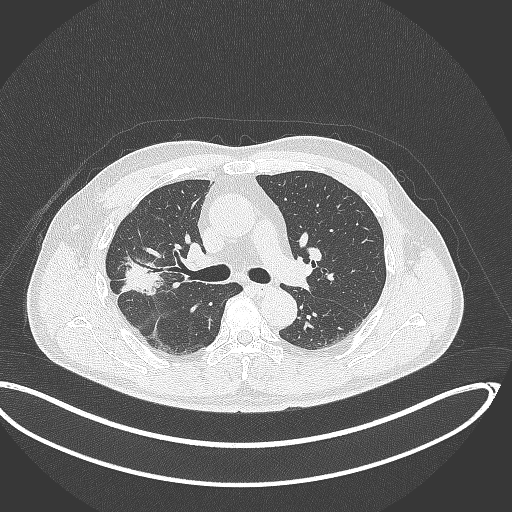
Chest CT, one axial slice; position 212 of 391 along the scan axis; 120 kVp; lung window (W 1500 / L -600 HU); 512 × 512 image matrix, field of view 439 × 439 mm. Patient: male, 63 years. From the clinical record (not read from this slice): clinical TNM (as recorded): T1c N0 M0.
Annotated regions visible in this slice (bounding box drawn by a radiologist):
- lung tumour (recorded histology: adenocarcinoma): box from (x=116, y=247) to (x=166, y=301) px